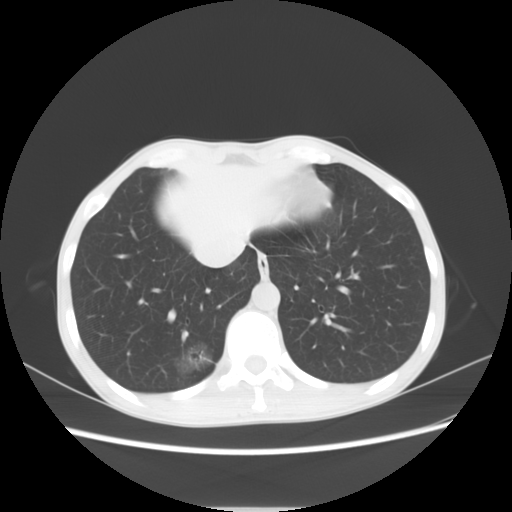
Chest CT, one axial slice. Position 20 of 69 along the scan axis. Reconstruction kernel STANDARD. 120 kVp. Lung window (W 1500 / L -600 HU). 5 mm slice thickness. 512 × 512 image matrix, field of view 350 × 350 mm. Patient: female, 51 years. Case-level facts recorded for this patient, not image findings: clinical TNM (as recorded): T1c N0 M0; histopathological grade: G2-3.
Structures marked on this image (rectangle marked by the reading radiologist):
- lung tumour (recorded histology: adenocarcinoma): box from (x=172, y=339) to (x=217, y=384) px